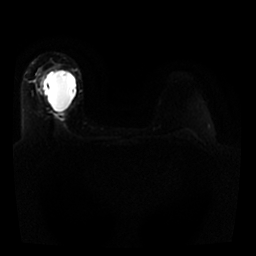
Breast MRI, one axial slice; slice 19 of 25 in the series (ordered by position); diffusion-weighted series; image 2 of 4 stored at this slice position (different b-values; order by instance number); 1.5 T; 256 × 256 image matrix. Female patient.
Structures marked on this image (manually delineated by an expert):
- tumour on diffusion-weighted imaging: bounding box [x1, y1, x2, y2] px = [41, 72, 49, 93]